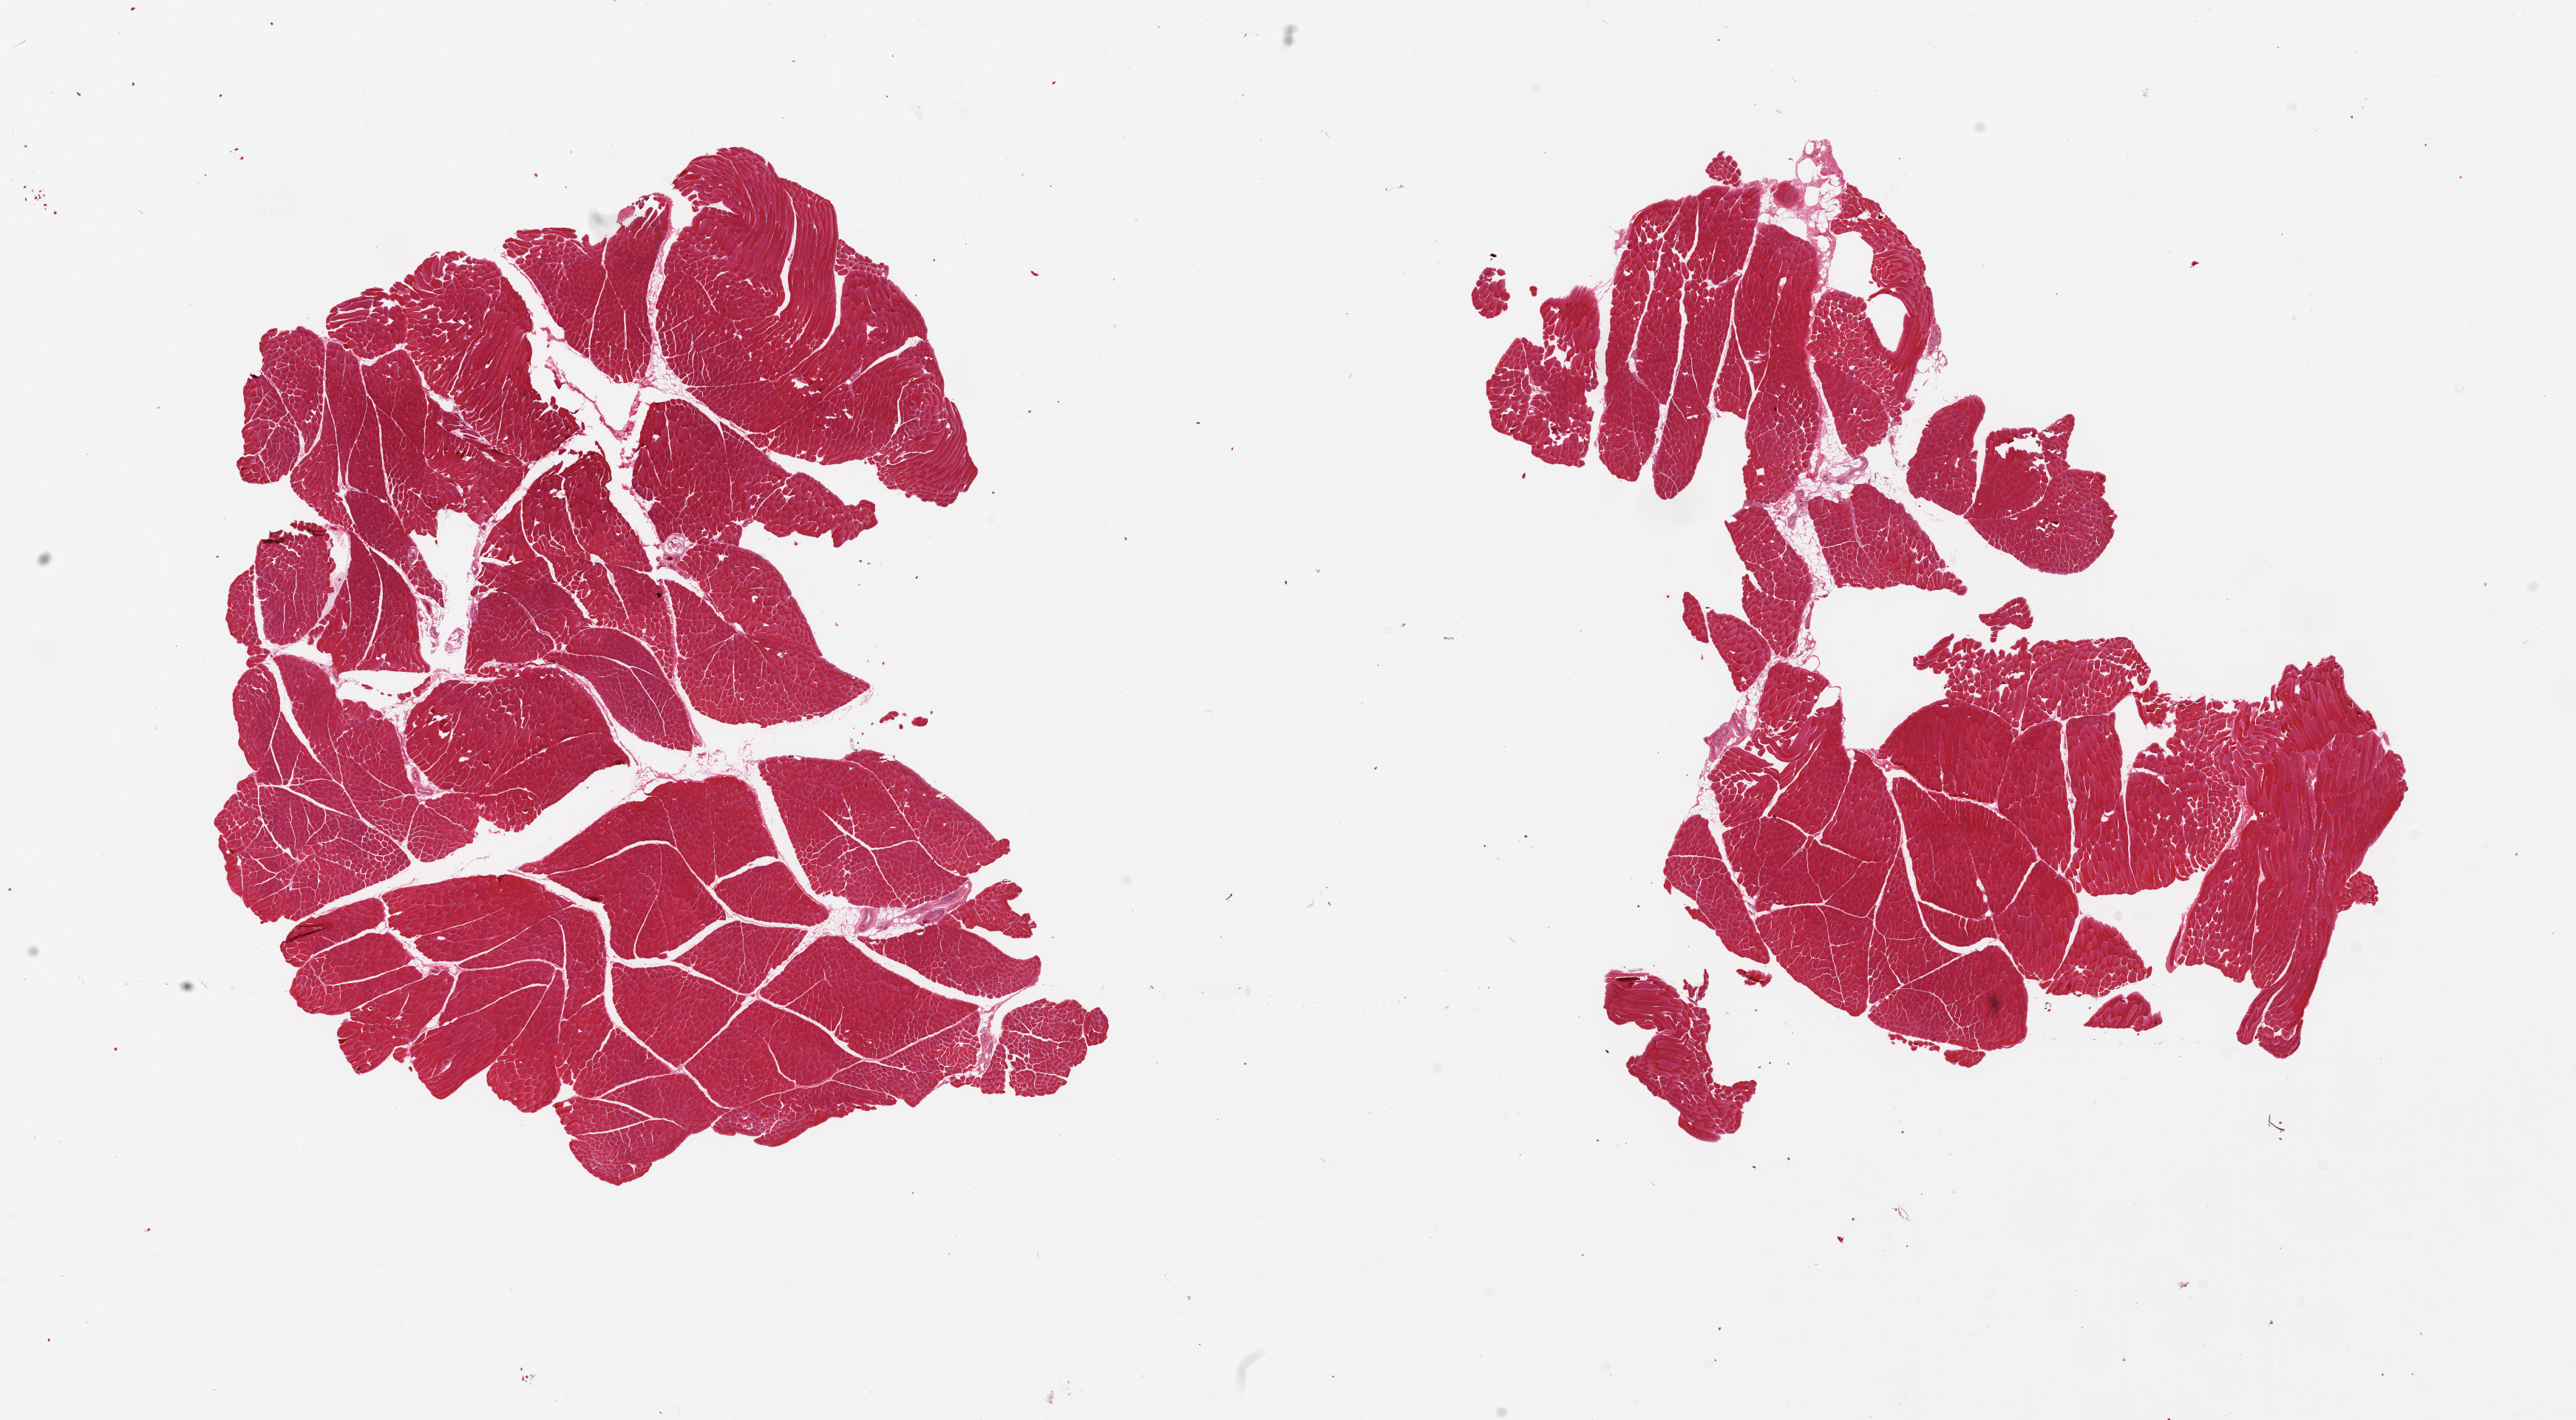
Whole-slide image, haematoxylin and eosin stain — a low-resolution overview of the entire scanned area, about 27.6 x 15.2 mm (from a 20x scan). PAXgene-fixed paraffin-embedded (PFPE) section. Target tissue: skeletal muscle. Donor tissue sample.
Reviewer comment on this tissue sample: 2 pieces, minimal internal adipose tissue.